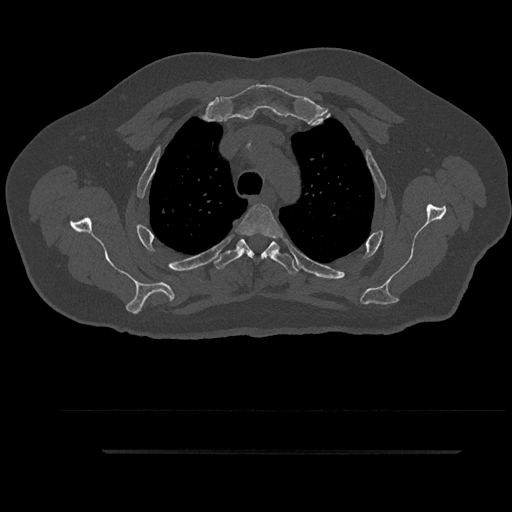
CT including the spine, one axial slice; position 695 of 797 along the scan axis; bone window (W 1800 / L 400 HU); 0.5 mm slice thickness; 512 × 512 image matrix. Male patient, age 63 years. Case-level facts recorded for this patient, not image findings: primary cancer: renal; vertebrae with lytic lesions (as recorded): T8.
Annotated regions visible in this slice (semi-automatically segmented with operator editing):
- T3 vertebra: bounding box <237,204,282,238> (left, top, right, bottom; pixels)
- T4 vertebra: <211,237,299,274>